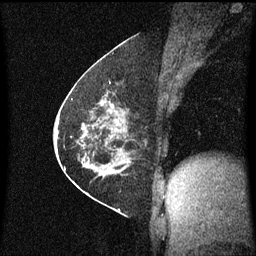
Breast MRI (dynamic contrast-enhanced), one sagittal slice. Position 31 of 60 along the scan axis. Dynamic contrast-enhanced series, image 2 of 3 at this slice position (ordered by acquisition). 1.5 T. TE 4.2 ms, TR 8.4 ms. 256 × 256 image matrix, field of view 200 × 200 mm. Patient: female, 60 years.
Structures marked on this image (semi-automatic segmentation, software-assisted and operator-edited):
- analysis volume of interest (the breast-tissue region the enhancement analysis was run in; not a lesion): bounding box [x1, y1, x2, y2] px = [69, 66, 144, 193]
- tumour enhancement mask (voxels above the 70 % enhancement threshold inside the analysis volume of interest): [69, 68, 131, 171]